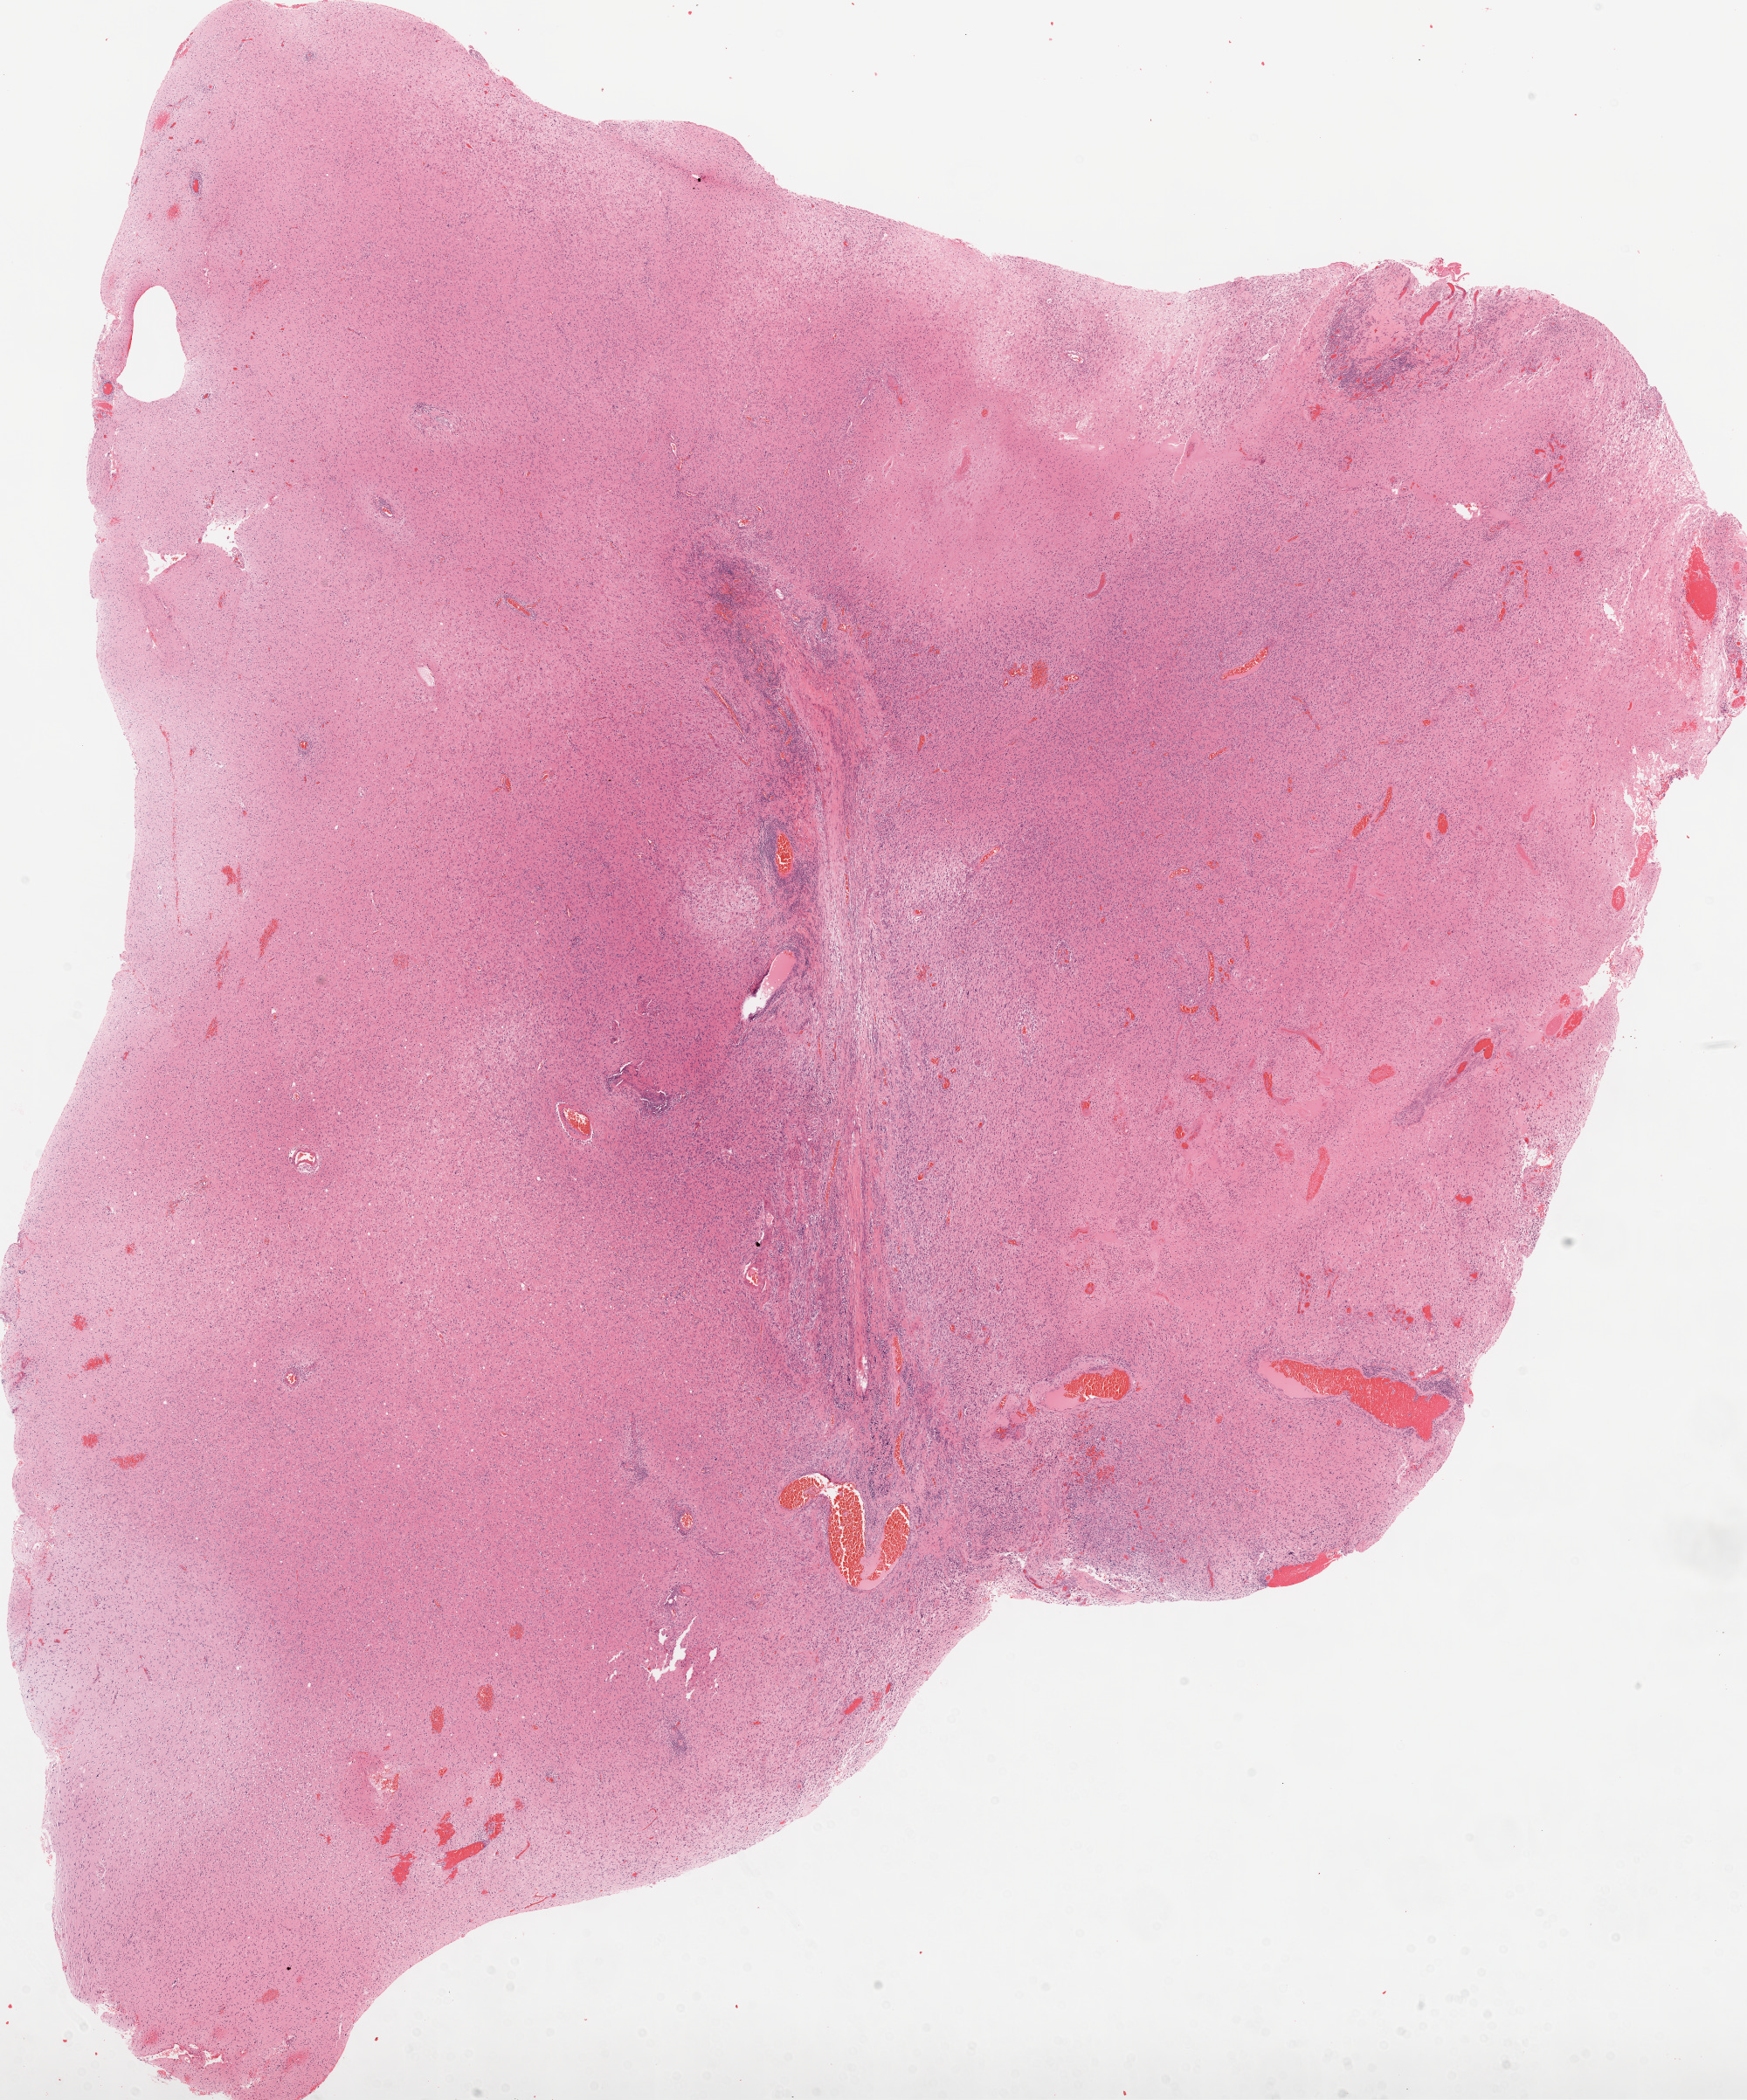
H&E-stained whole-slide image, a low-resolution overview of the entire scanned area, about 16.0 x 19.3 mm; FFPE section; primary tumour sample from the brain. Female, age 20 years at initial diagnosis.
* histologic diagnosis: Glioblastoma